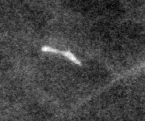
Cropped region of a digitized screen-film mammogram centred on a radiologist-marked abnormality, left breast, MLO view.
Finding: calcifications, distribution regional; BI-RADS assessment category 2; subtlety rating 3 on a 1 (subtle) to 5 (obvious) scale; benign without callback (not worked up further).